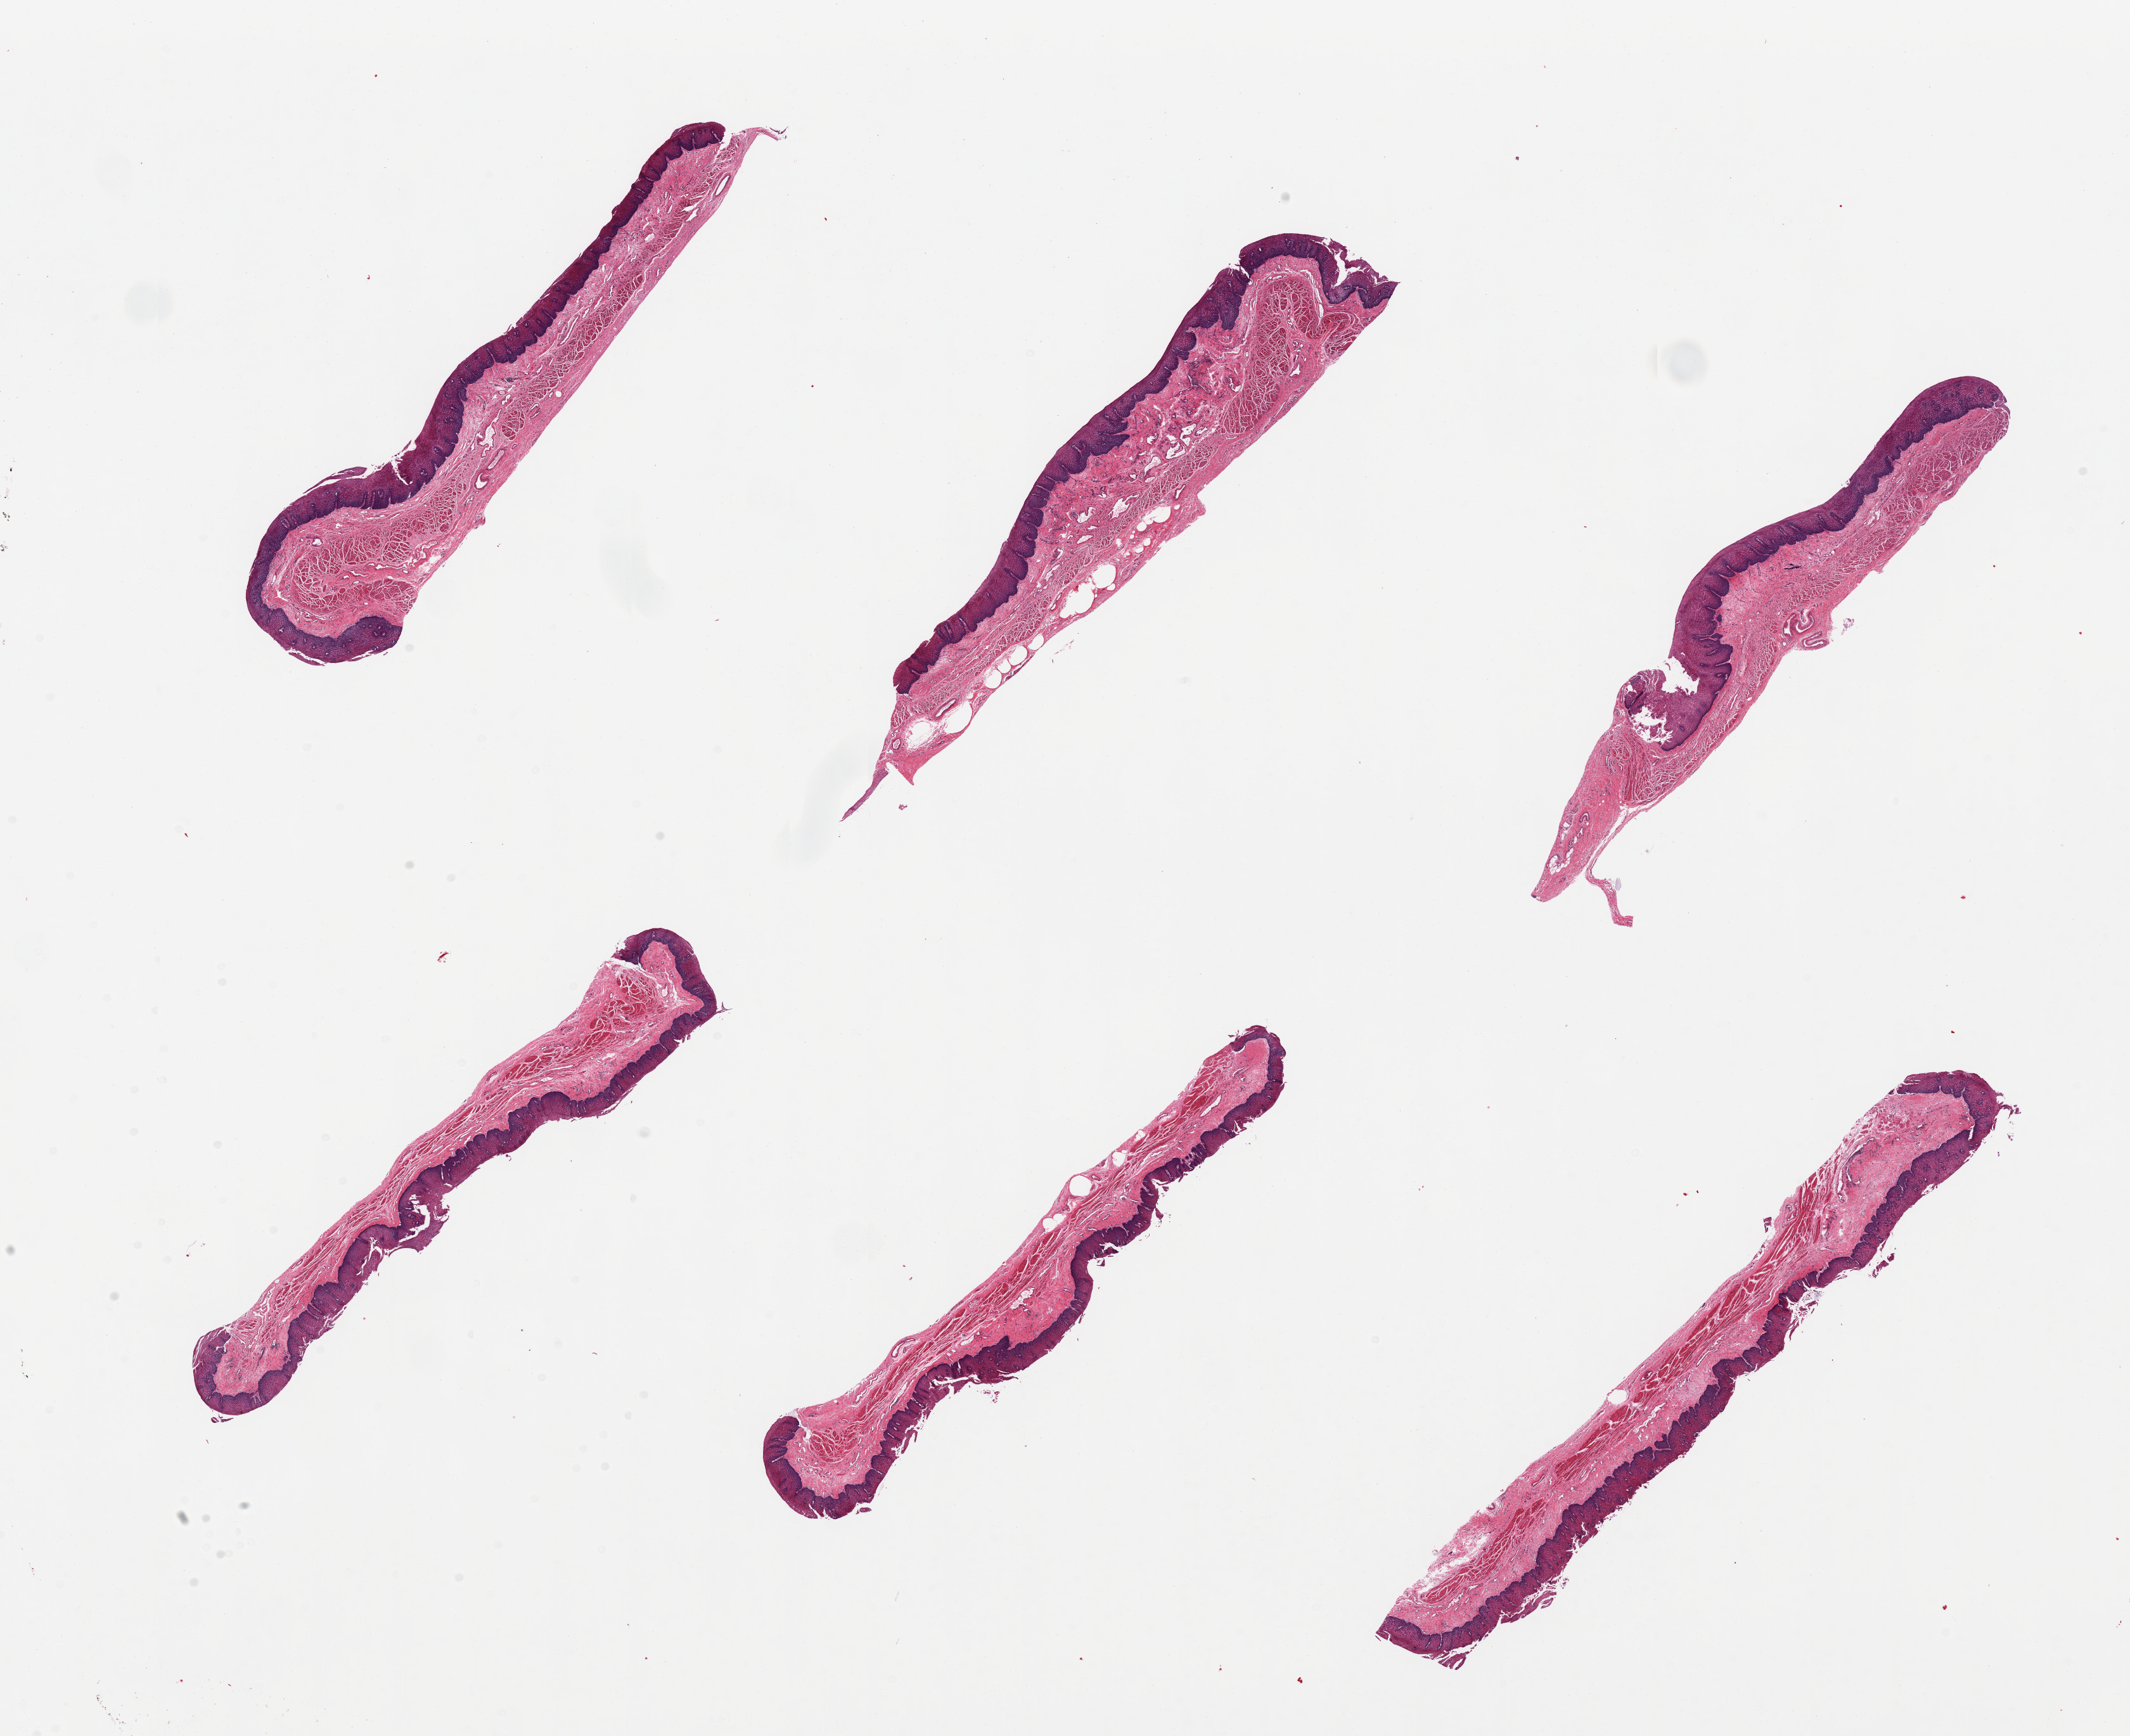
Digitized hematoxylin and eosin (H&E)-stained section, a low-resolution overview of the entire scanned area, about 26.6 x 21.7 mm. PAXgene-fixed, paraffin-embedded tissue. Target tissue: esophageal mucous membrane. Donor tissue sample. Donor: female.
Review note (as recorded): 6 pieces, squamous mucosa is ~0.3mm, ~25-30% thickness.